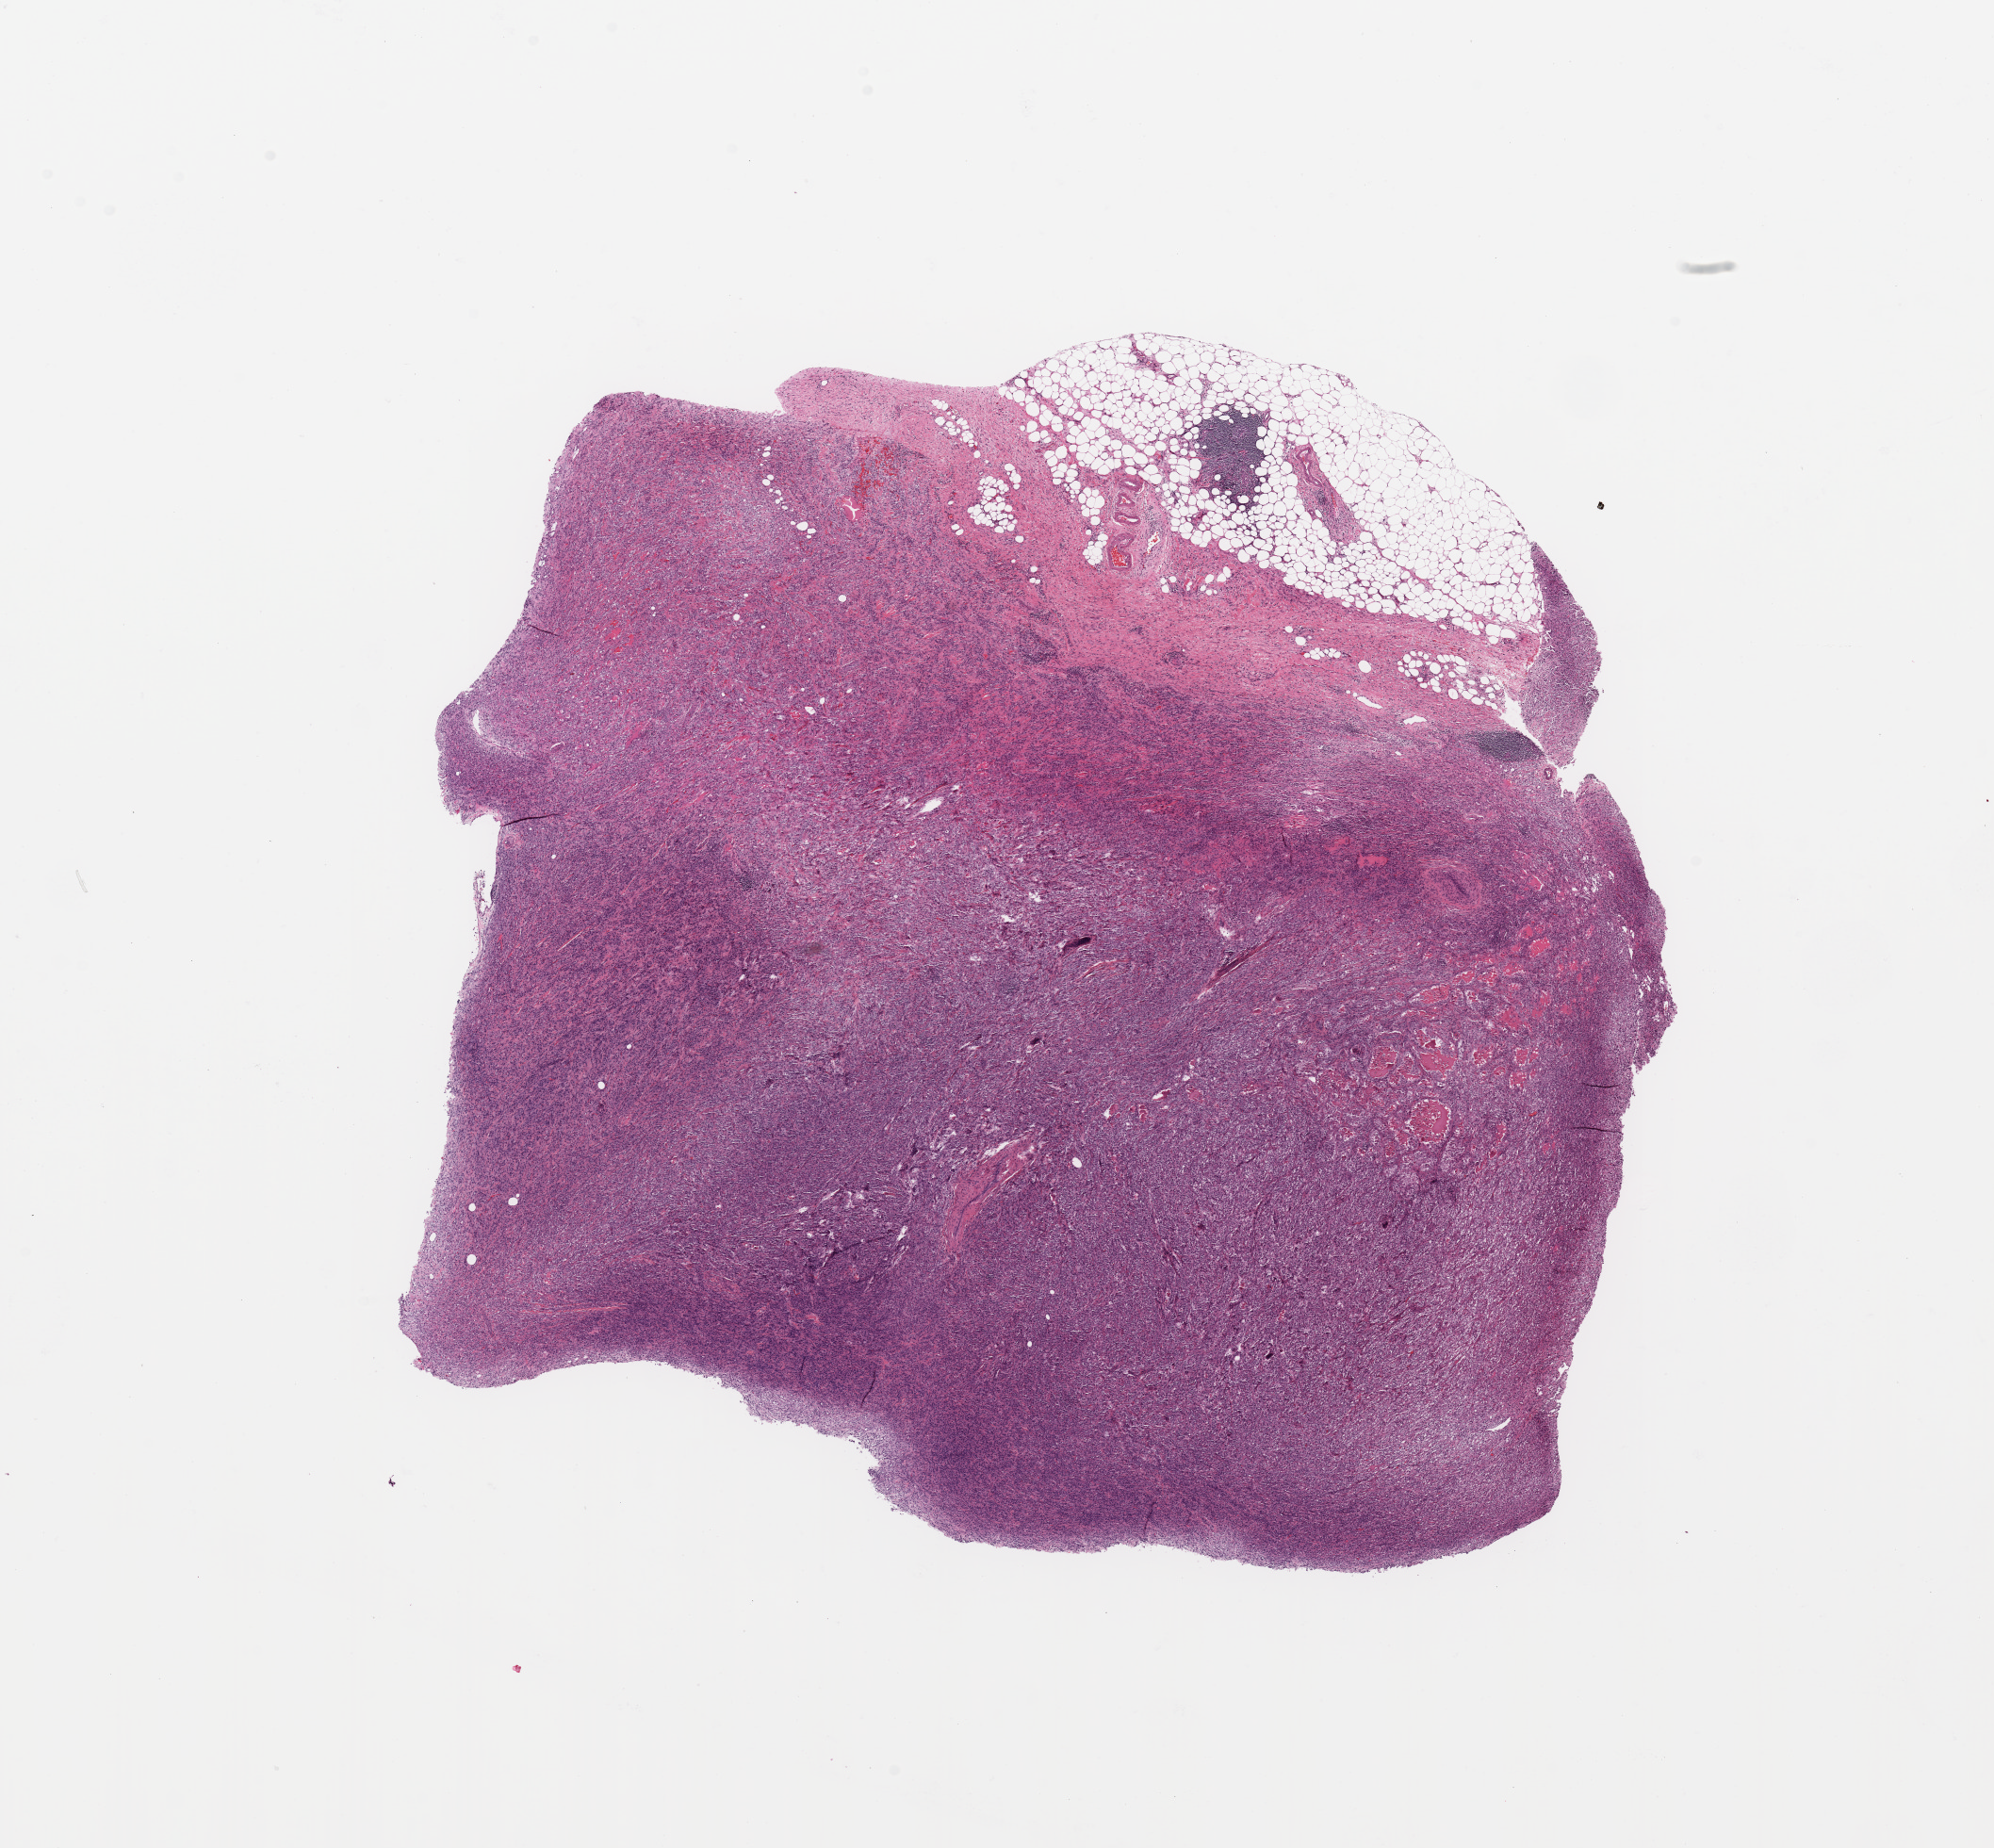
H&E-stained whole-slide image, a low-resolution overview of the entire scanned area, about 16.7 x 15.5 mm (acquisition: 20x scan). Kidney, tumour tissue. Male, 61 y/o. Histologic grade: G4 (undifferentiated).
- AJCC pathologic stage: IV
- primary tumour site (as recorded): upper pole
- diagnosis: Renal cell carcinoma, NOS